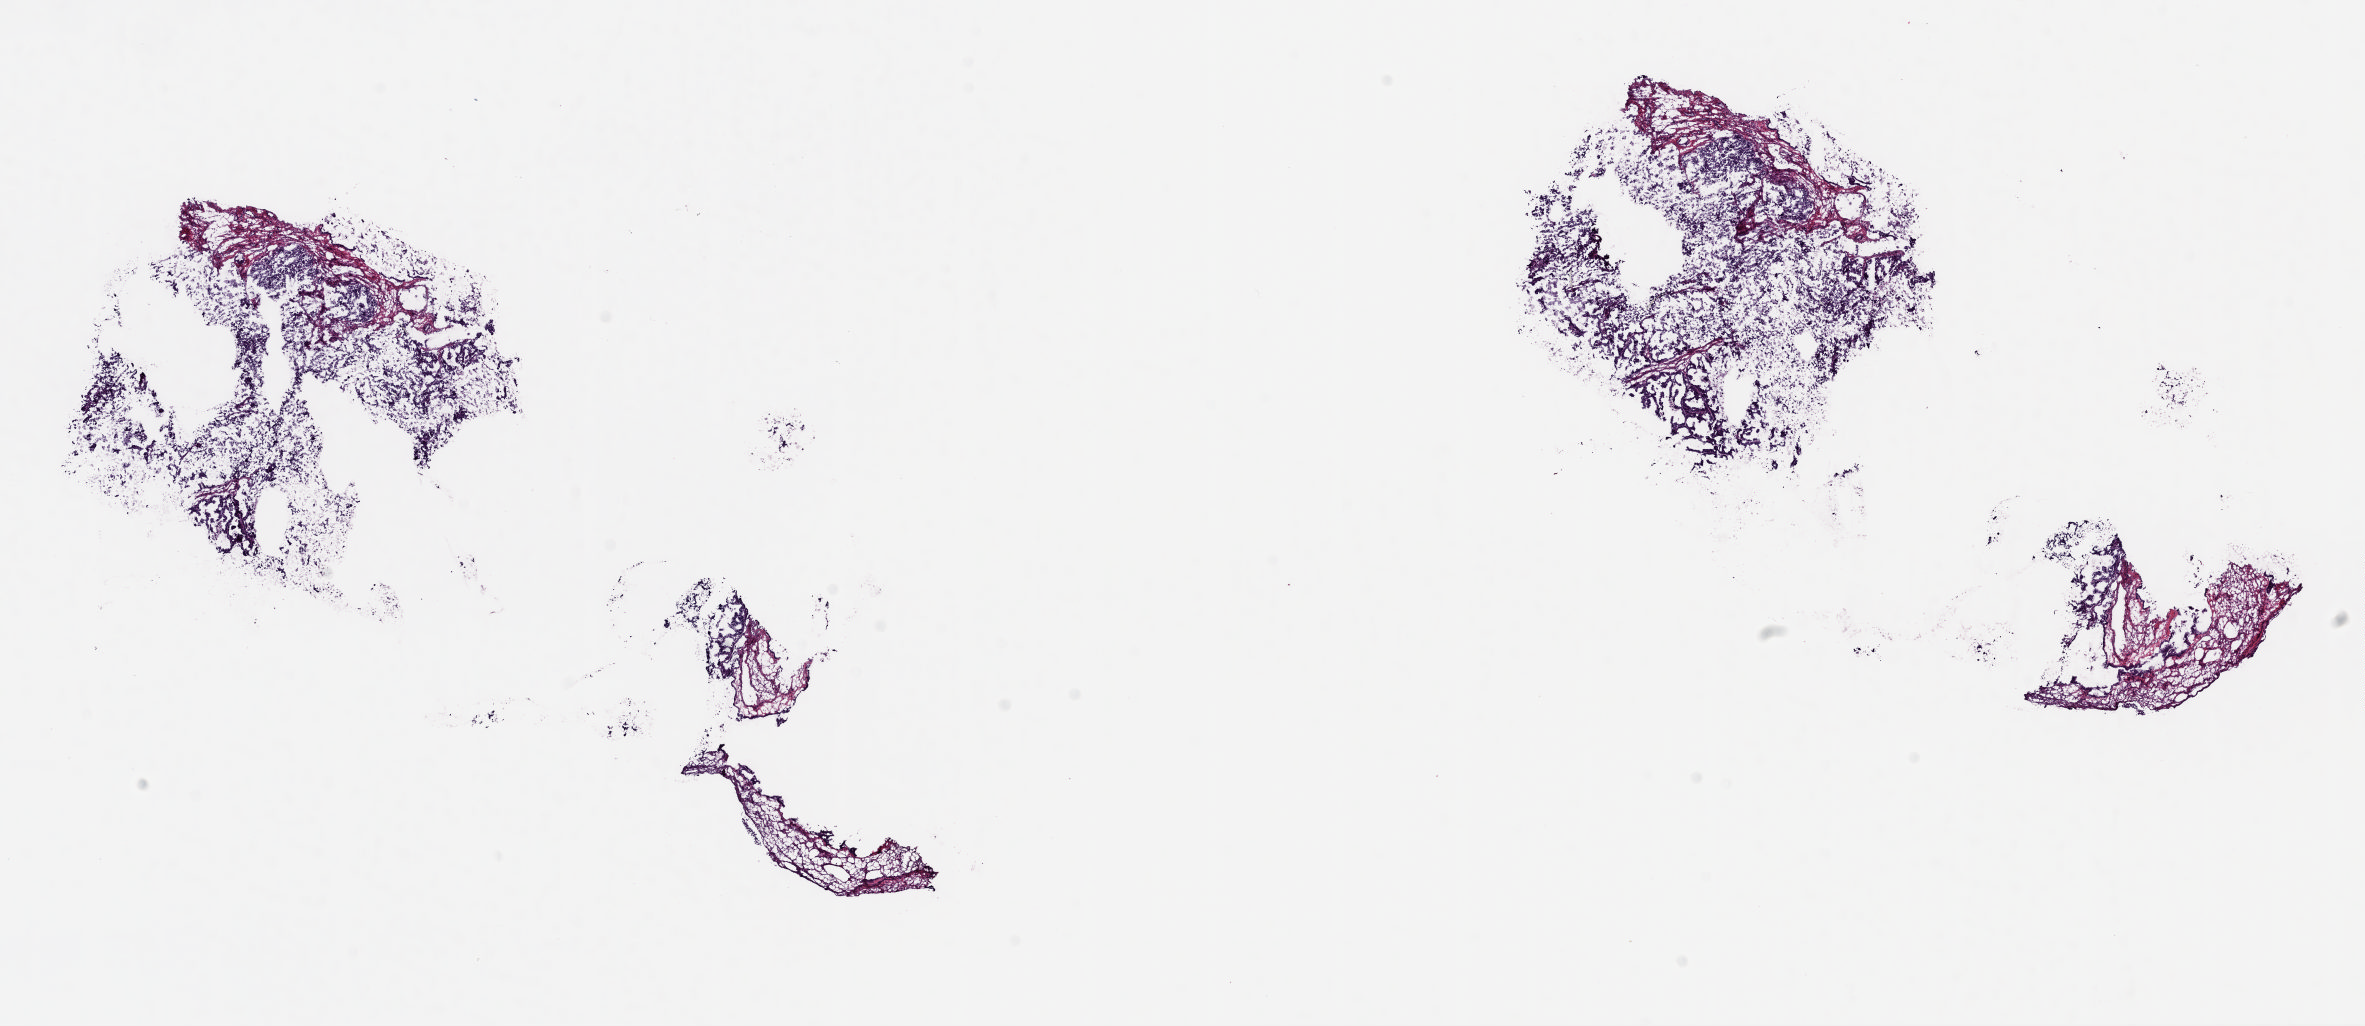
Digitized Hematoxylin and eosin (H&E) stained tissue section (whole slide) — shown as a low-resolution overview of the whole scanned area (about 18.7 x 8.1 mm). Frozen section from the top of the tissue portion. Uterus, primary tumour sample. Female, age 68 years at initial diagnosis. Histologic grade: high grade. Pathologist review of this section (percent, as recorded): tumour cells 65%, tumour nuclei 65%, normal cells 0%, stromal cells 35%, necrosis 0%. Inflammatory infiltration, as recorded: lymphocyte infiltration 0%, monocyte infiltration 0%, neutrophil infiltration 0%.
Lymph nodes positive (case pathology): 0 of 10 examined. FIGO stage: IA. Histologic diagnosis: Serous cystadenocarcinoma, NOS (endometrium).